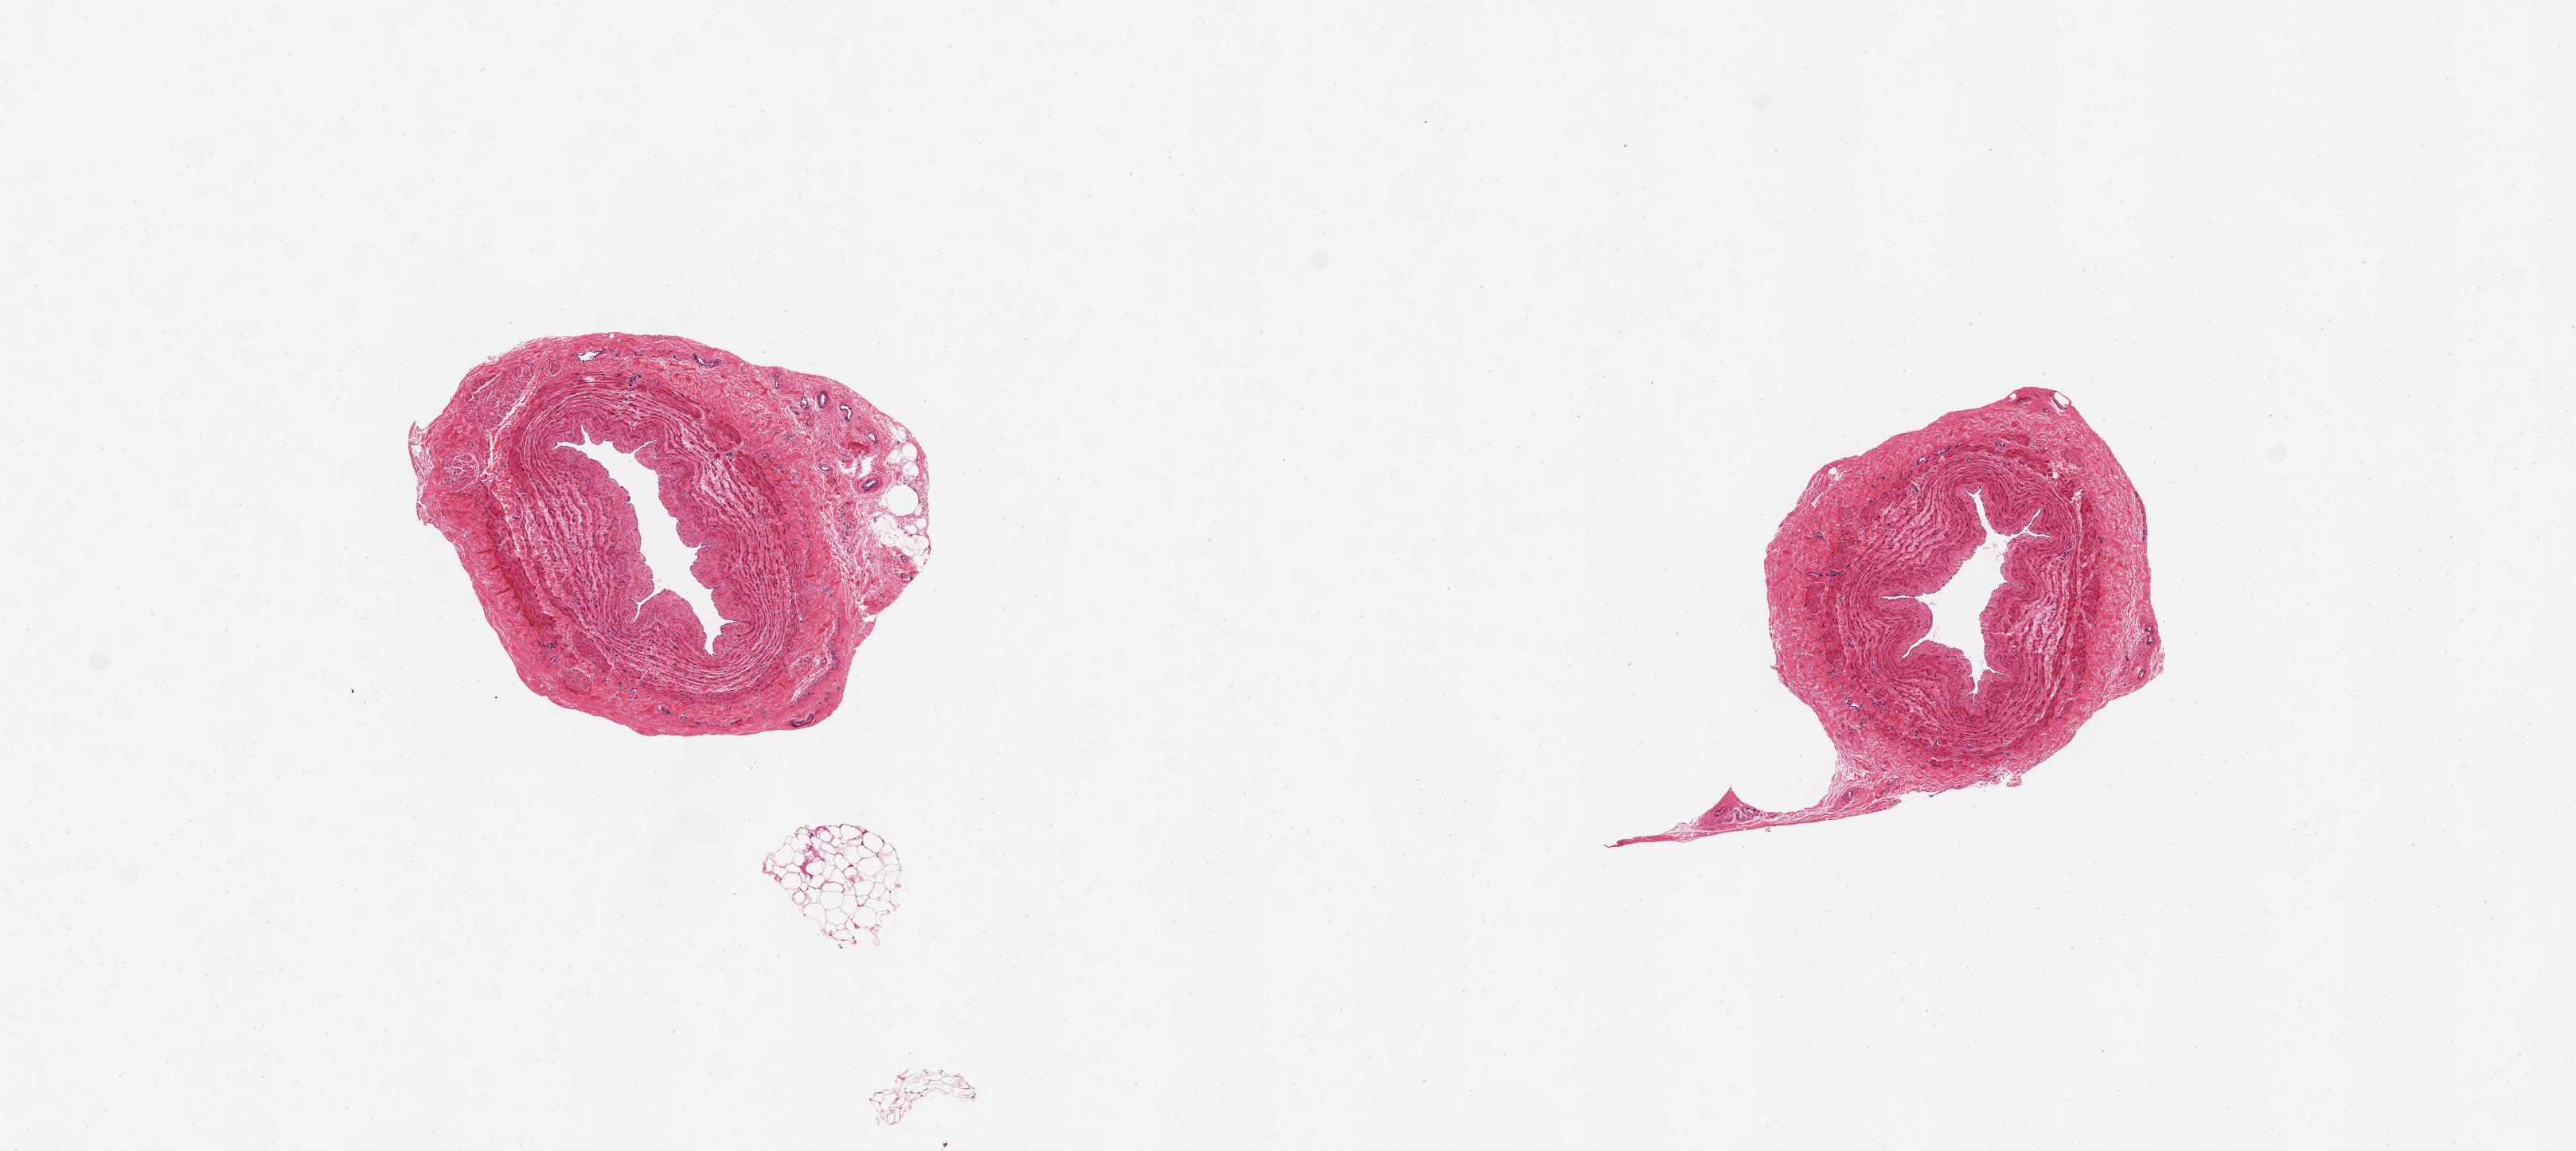
Whole-slide image, hematoxylin and eosin (H&E) stain, low-resolution overview of the scanned area, about 12.8 x 5.7 mm (from a 20x scan), PAXgene-fixed, paraffin-embedded tissue, sampled site (target tissue): tibial artery, tissue donor sample. Donor sex: female.
* review note (as recorded): 2 pieces 2 mm in diameter; normal arteries minimal adipose tissue